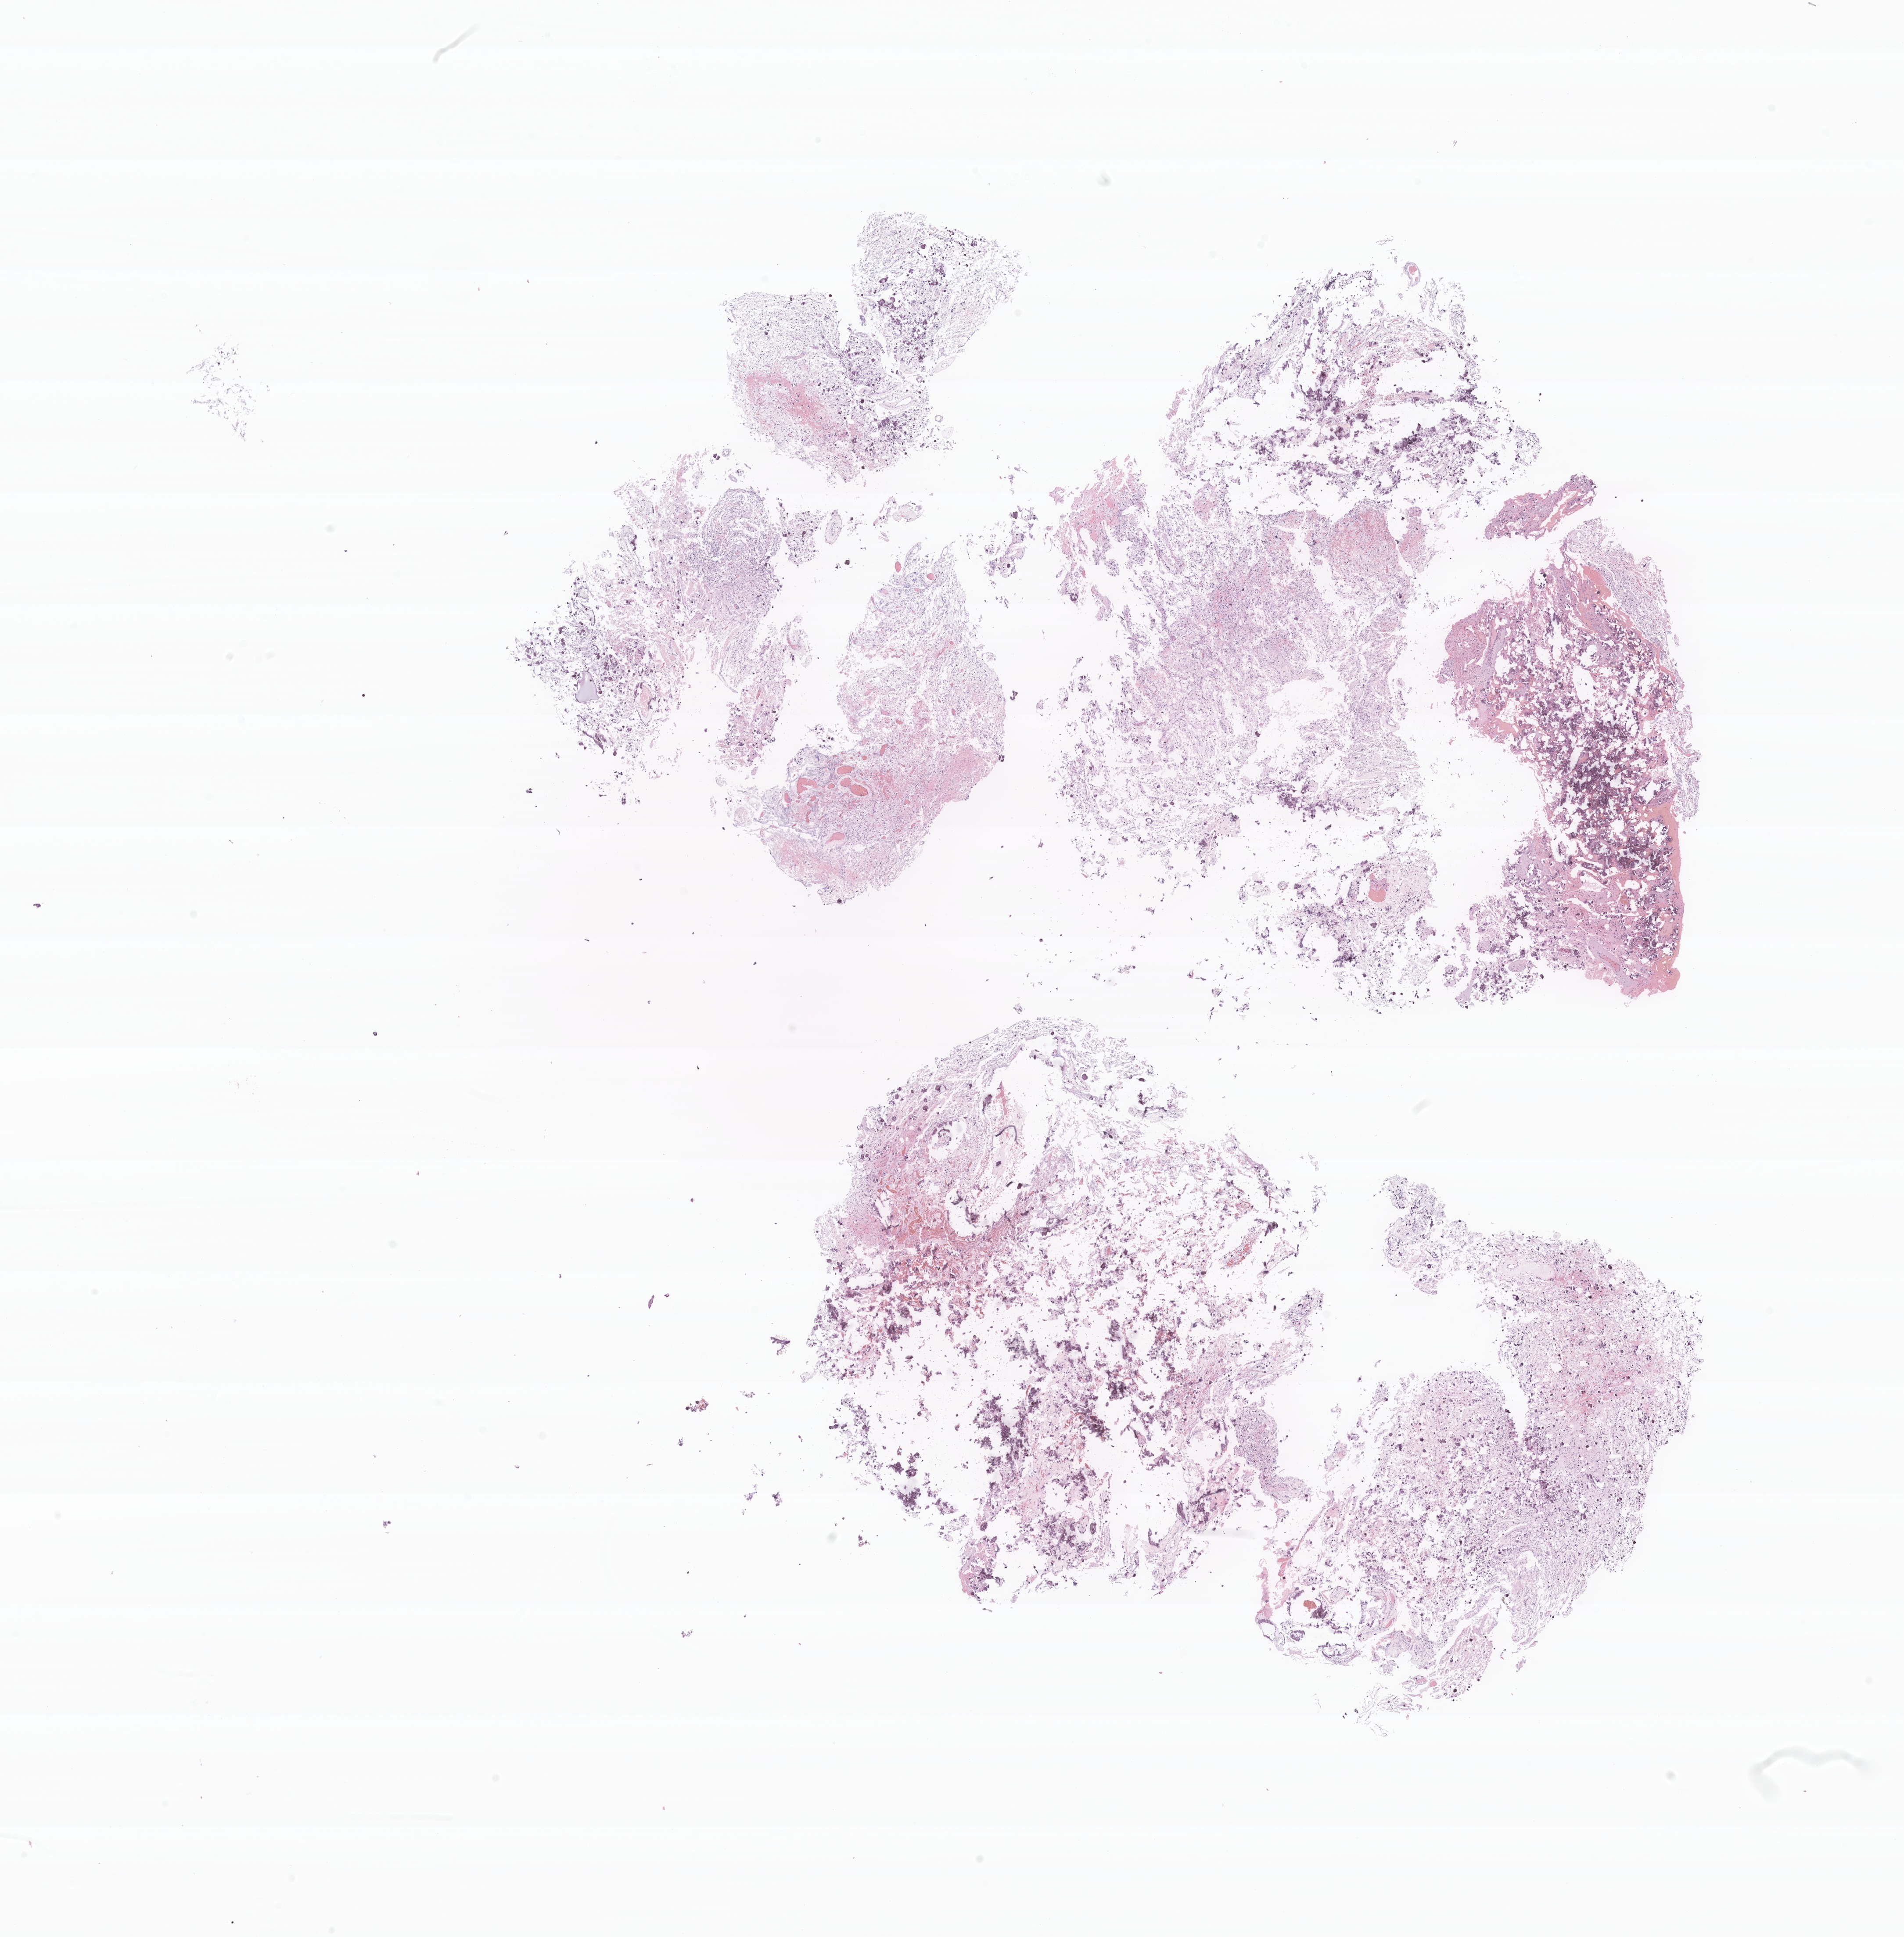
Whole-slide image, hematoxylin and eosin (H&E) stain of tumor tissue from the spinal cord, low-resolution overview of the scanned area, about 18.2 x 18.6 mm. Formalin-fixed paraffin-embedded section. Female patient, age 204 months.
Diagnosis: Ganglioglioma, NOS.